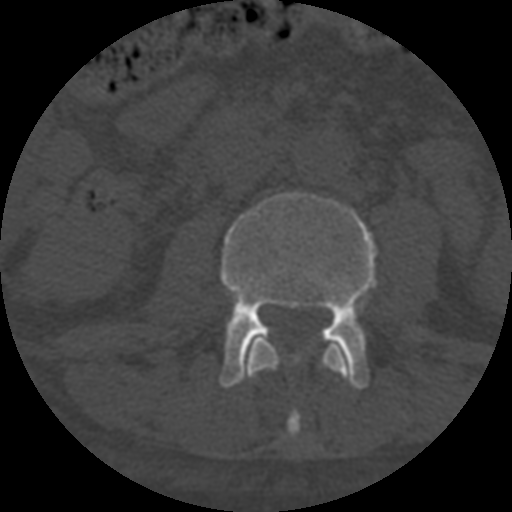
CT including the spine, one axial slice. Slice 242 of 708 in the series (ordered by position). Reconstruction kernel STANDARD. One of 3 acquisitions stored at this slice position. Bone window (W 1800 / L 400 HU). 1.25 mm slice thickness. 512 × 512 image matrix. Patient age 55 years. From the clinical record (not read from this slice): primary cancer: colon.
Structures marked on this image (semi-automatic segmentation, software-assisted and operator-edited):
- L2 vertebra: bounding box <245,337,347,439> (left, top, right, bottom; pixels)
- L3 vertebra: <160,191,410,389>